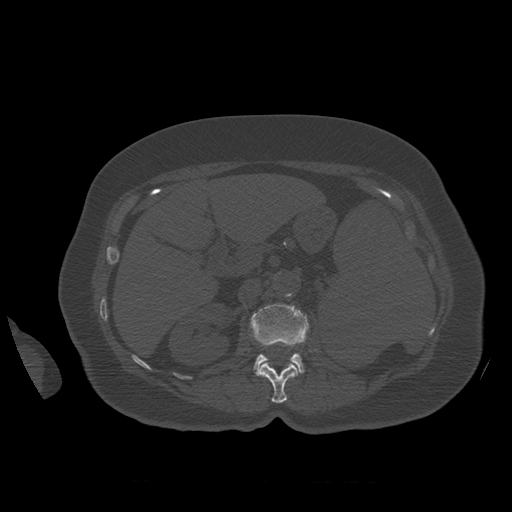
CT including the spine, one axial slice; position 266 of 399 along the scan axis; 120 kVp; bone window (W 1800 / L 400 HU); 1.25 mm slice thickness; 512 × 512 image matrix, field of view 404 × 404 mm. Patient age 81 years. From the clinical record (not read from this slice): primary cancer: renal; vertebrae with lytic lesions (as recorded): L1.
Structures marked on this image (semi-automatically segmented with operator editing):
- L1 vertebra: bounding box [x1, y1, x2, y2] px = [260, 363, 298, 404]
- L2 vertebra: [251, 304, 310, 376]